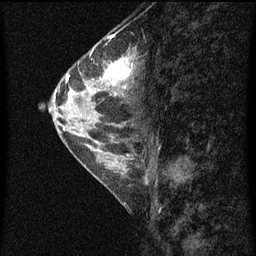
Breast MRI (dynamic contrast-enhanced), one sagittal slice. Position 28 of 60 along the scan axis. Dynamic contrast-enhanced series, image 2 of 4 at this slice position (ordered by acquisition). 1.5 T. TE 4.2 ms, TR 8 ms. 2 mm slice thickness. 256 × 256 image matrix. Female patient, age 56 years.
Outlined on this slice (semi-automatic segmentation, software-assisted and operator-edited):
- analysis volume of interest (the breast-tissue region the enhancement analysis was run in; not a lesion): bounding box (x1, y1, x2, y2) in pixels: (56, 52, 136, 115)
- tumour enhancement mask (voxels above the 70 % enhancement threshold inside the analysis volume of interest): (67, 58, 131, 103)